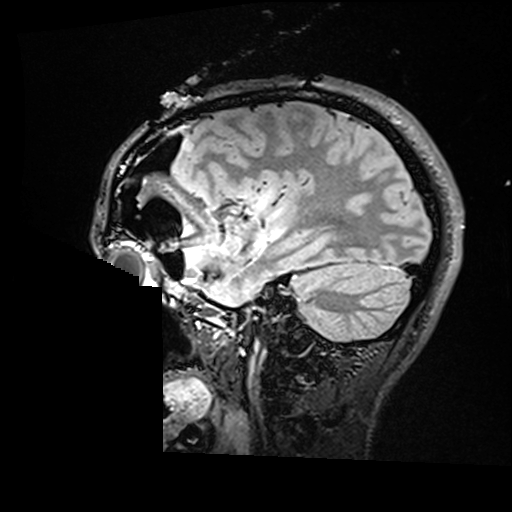
Brain MRI from a brain-tumour surgery series, one sagittal slice; slice 120 of 176 in the series (ordered by position); T2 FLAIR; 1 mm slice thickness; 512 × 512 image matrix. Case-level facts recorded for this patient, not image findings: histopathology: Astrocytoma; WHO grade: 2; IDH mutation: yes; tumour location: Right Insular.
Outlined on this slice (expert manual segmentation):
- residual tumour: box from (x=257, y=190) to (x=279, y=220) px